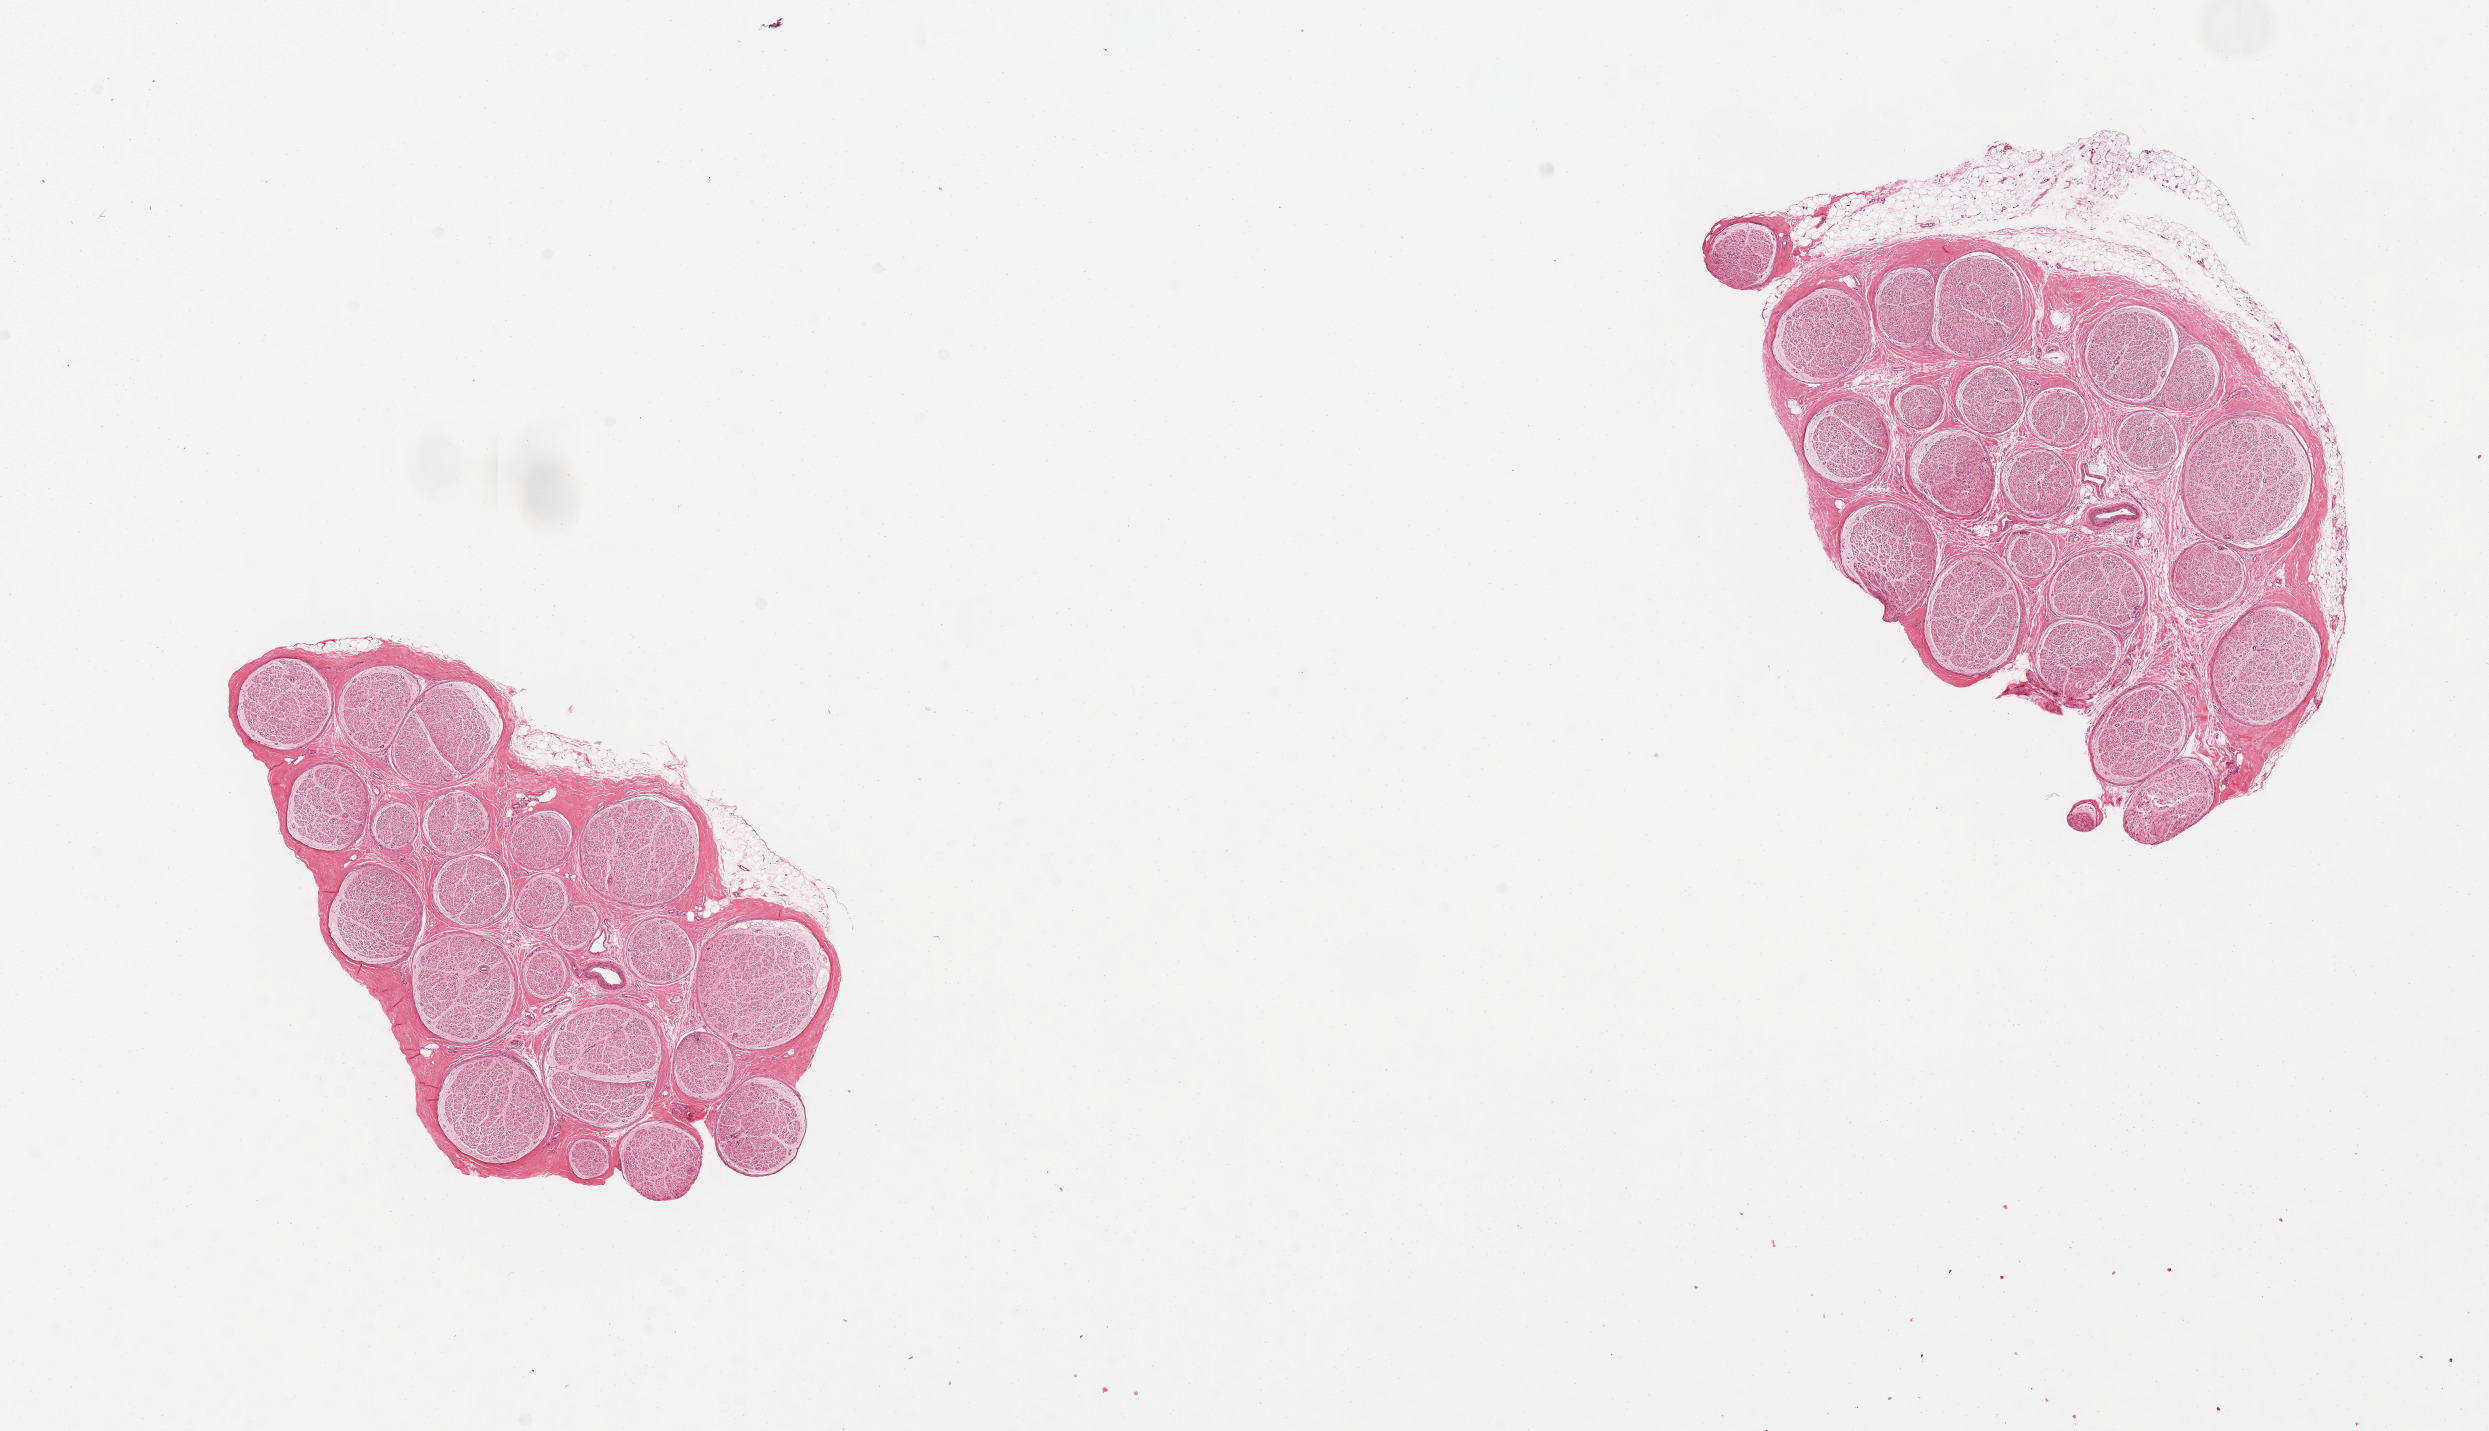
Digitized haematoxylin and eosin-stained section, brightfield — a low-resolution overview of the entire scanned area, about 19.7 x 11.3 mm (from a 20x scan). PAXgene-fixed, paraffin-embedded tissue. Section of tibial nerve (target tissue). Donor tissue sample. Male donor.
Pathologist's review note for this sample: 2 pieces; 10% external; fat.